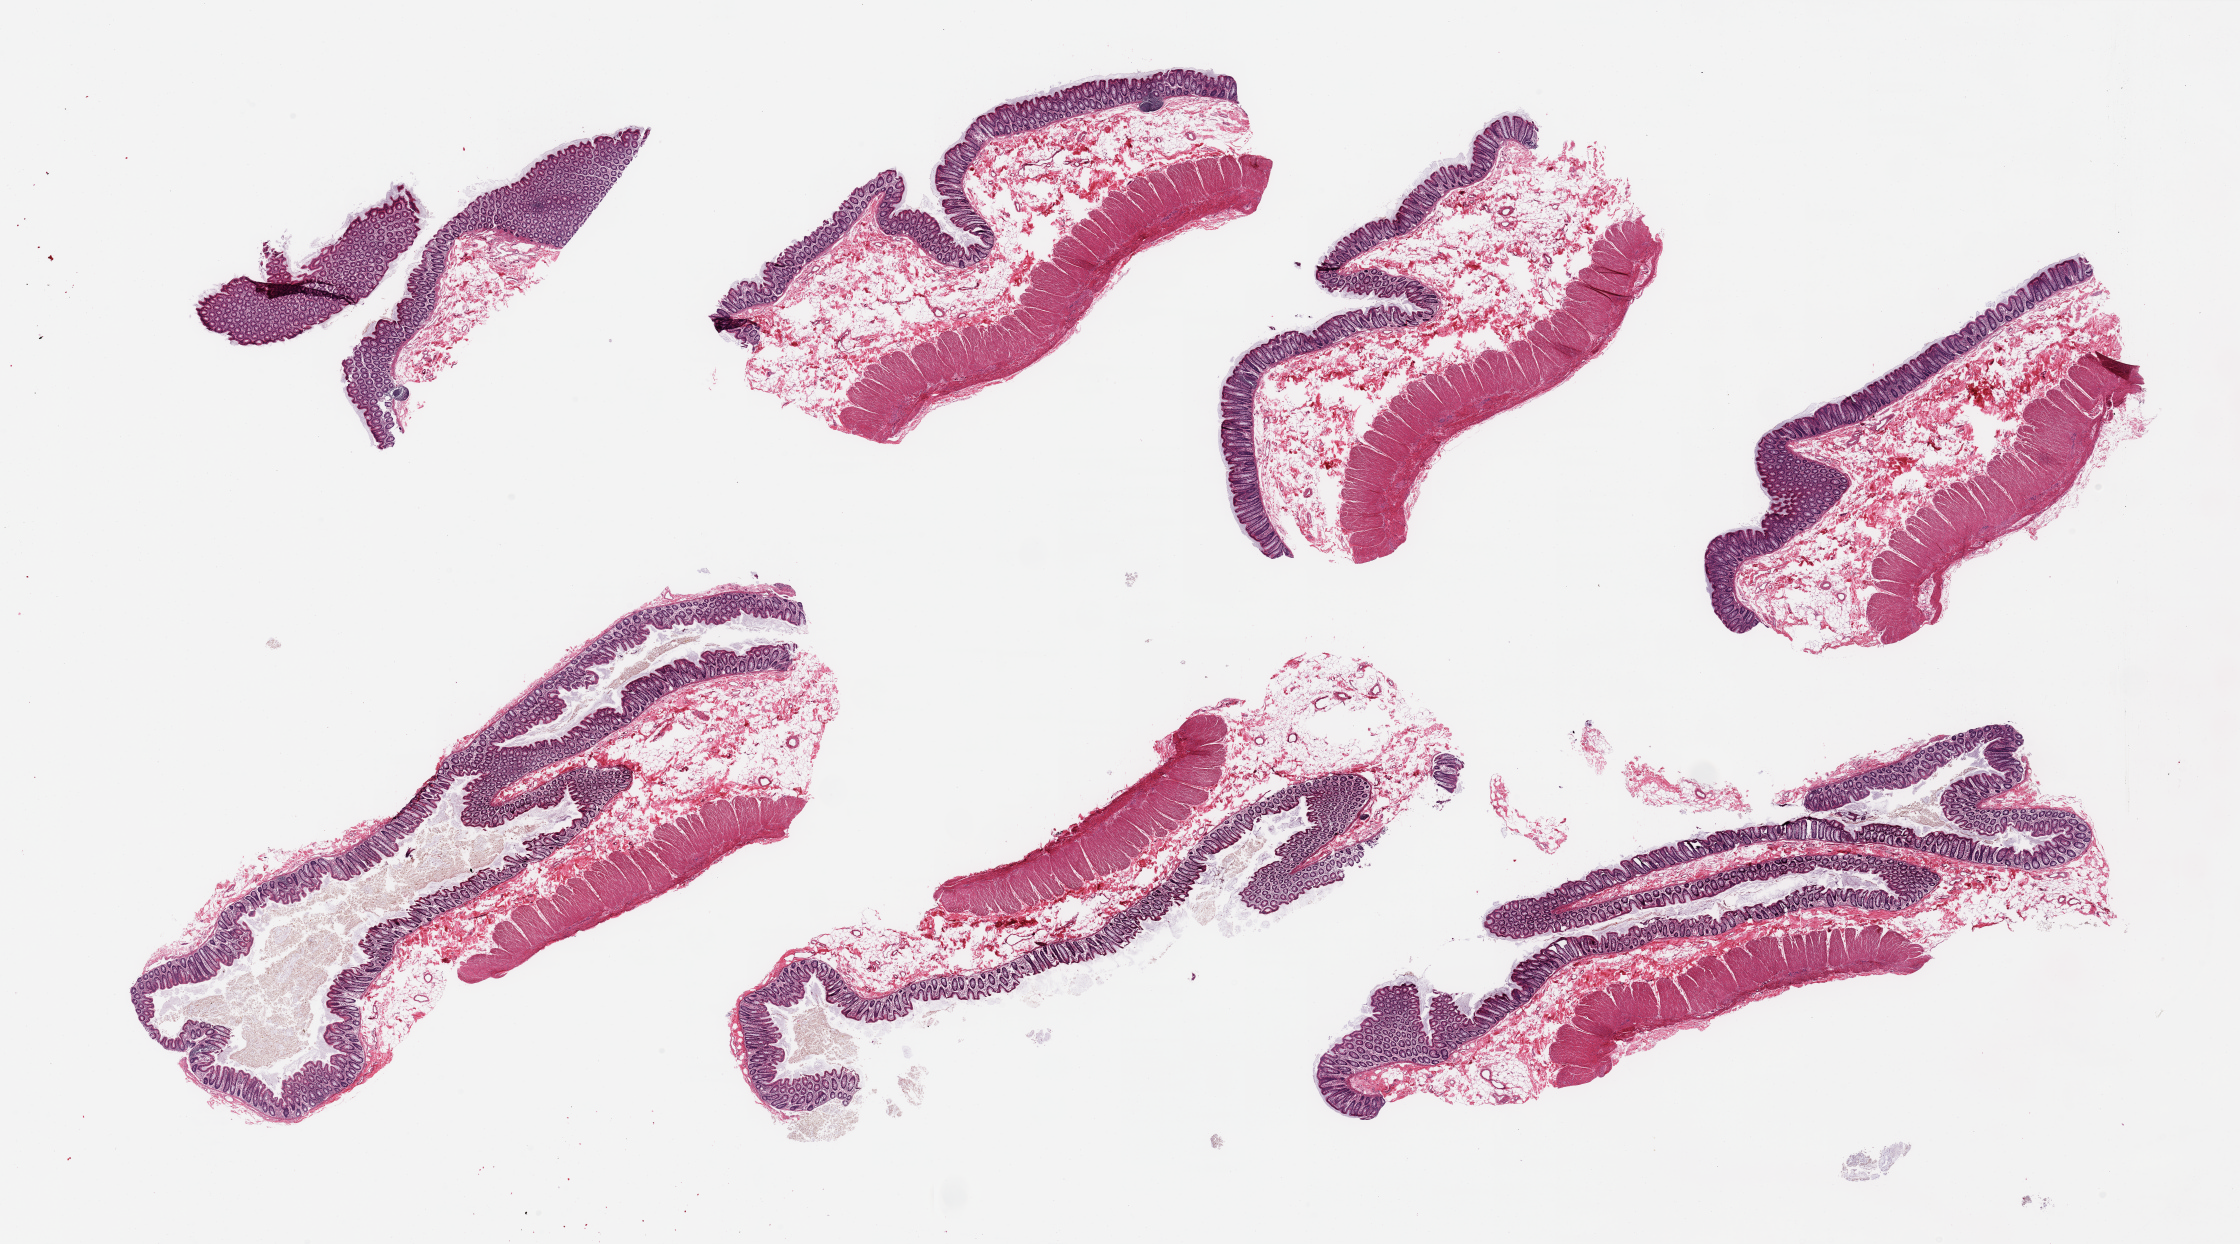
Whole-slide image, haematoxylin and eosin stain — whole scanned area (about 35.4 x 19.7 mm, slide scanned at 20x) shown as a low-resolution overview, PAXgene-fixed, paraffin-embedded tissue, sampled site (target tissue): transverse colon, tissue donor sample. Donor sex: male.
Pathologist's review note for this sample: 7 pieces; mild to moderate autolysis.